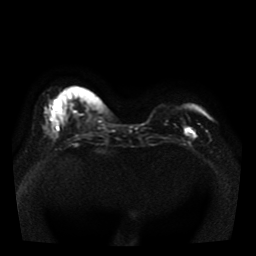
Breast MRI, one axial slice. Position 13 of 41 along the scan axis. Diffusion-weighted series; image 2 of 4 stored at this slice position (different b-values; order by instance number). 1.5 T. 5 mm slice thickness. 256 × 256 image matrix, field of view 330 × 330 mm. Female patient.
Annotated regions visible in this slice (expert manual segmentation):
- tumour on diffusion-weighted imaging: bounding box <184,128,196,138> (left, top, right, bottom; pixels)